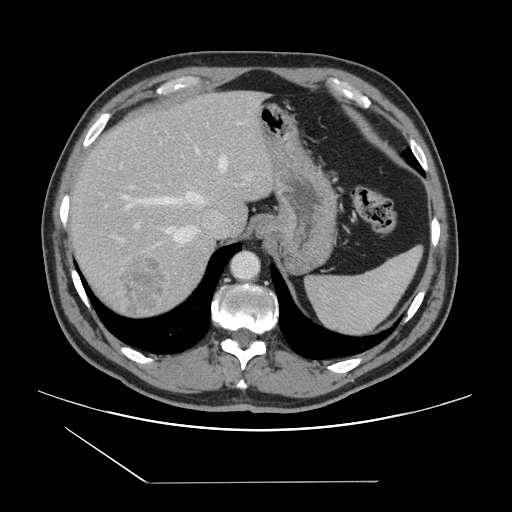
Contrast-enhanced abdominal CT, one axial slice; position 115 of 157 along the scan axis; intravenous contrast given; soft-tissue window (W 400 / L 40 HU); 512 × 512 image matrix, field of view 407 × 407 mm. Male patient, age 61 years. Case-level facts recorded for this patient, not image findings: diagnosis: colorectal cancer liver metastases, imaged before liver resection; multiple liver metastases: yes; largest metastasis: 5.5 cm; chemotherapy before resection: no.
Structures marked on this image (outlined manually by an expert reader):
- hepatic veins: bounding box (x1, y1, x2, y2) in pixels: (121, 148, 227, 247)
- liver: (69, 92, 275, 317)
- planned liver remnant (the part of the liver to remain after resection): (70, 92, 236, 231)
- portal vein (with intrahepatic branches): (119, 143, 251, 241)
- liver metastasis: (119, 251, 170, 319)